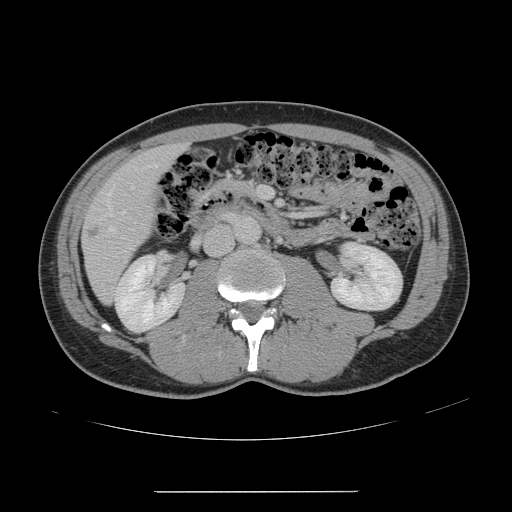
Contrast-enhanced abdominal CT, one axial slice. Slice 52 of 178 in the series (ordered by position). Soft-tissue window (W 400 / L 40 HU). 512 × 512 image matrix, field of view 401 × 401 mm. Male patient, age 53 years. Case-level facts recorded for this patient, not image findings: diagnosis: colorectal cancer liver metastases, imaged before liver resection; multiple liver metastases: yes; largest metastasis: 2.4 cm; disease in both lobes: no.
Structures marked on this image (manually delineated by an expert):
- hepatic veins: bounding box <101,165,158,233> (left, top, right, bottom; pixels)
- liver: <83,147,179,300>
- portal vein (with intrahepatic branches): <259,186,267,199>
- liver metastasis: <88,228,99,238>